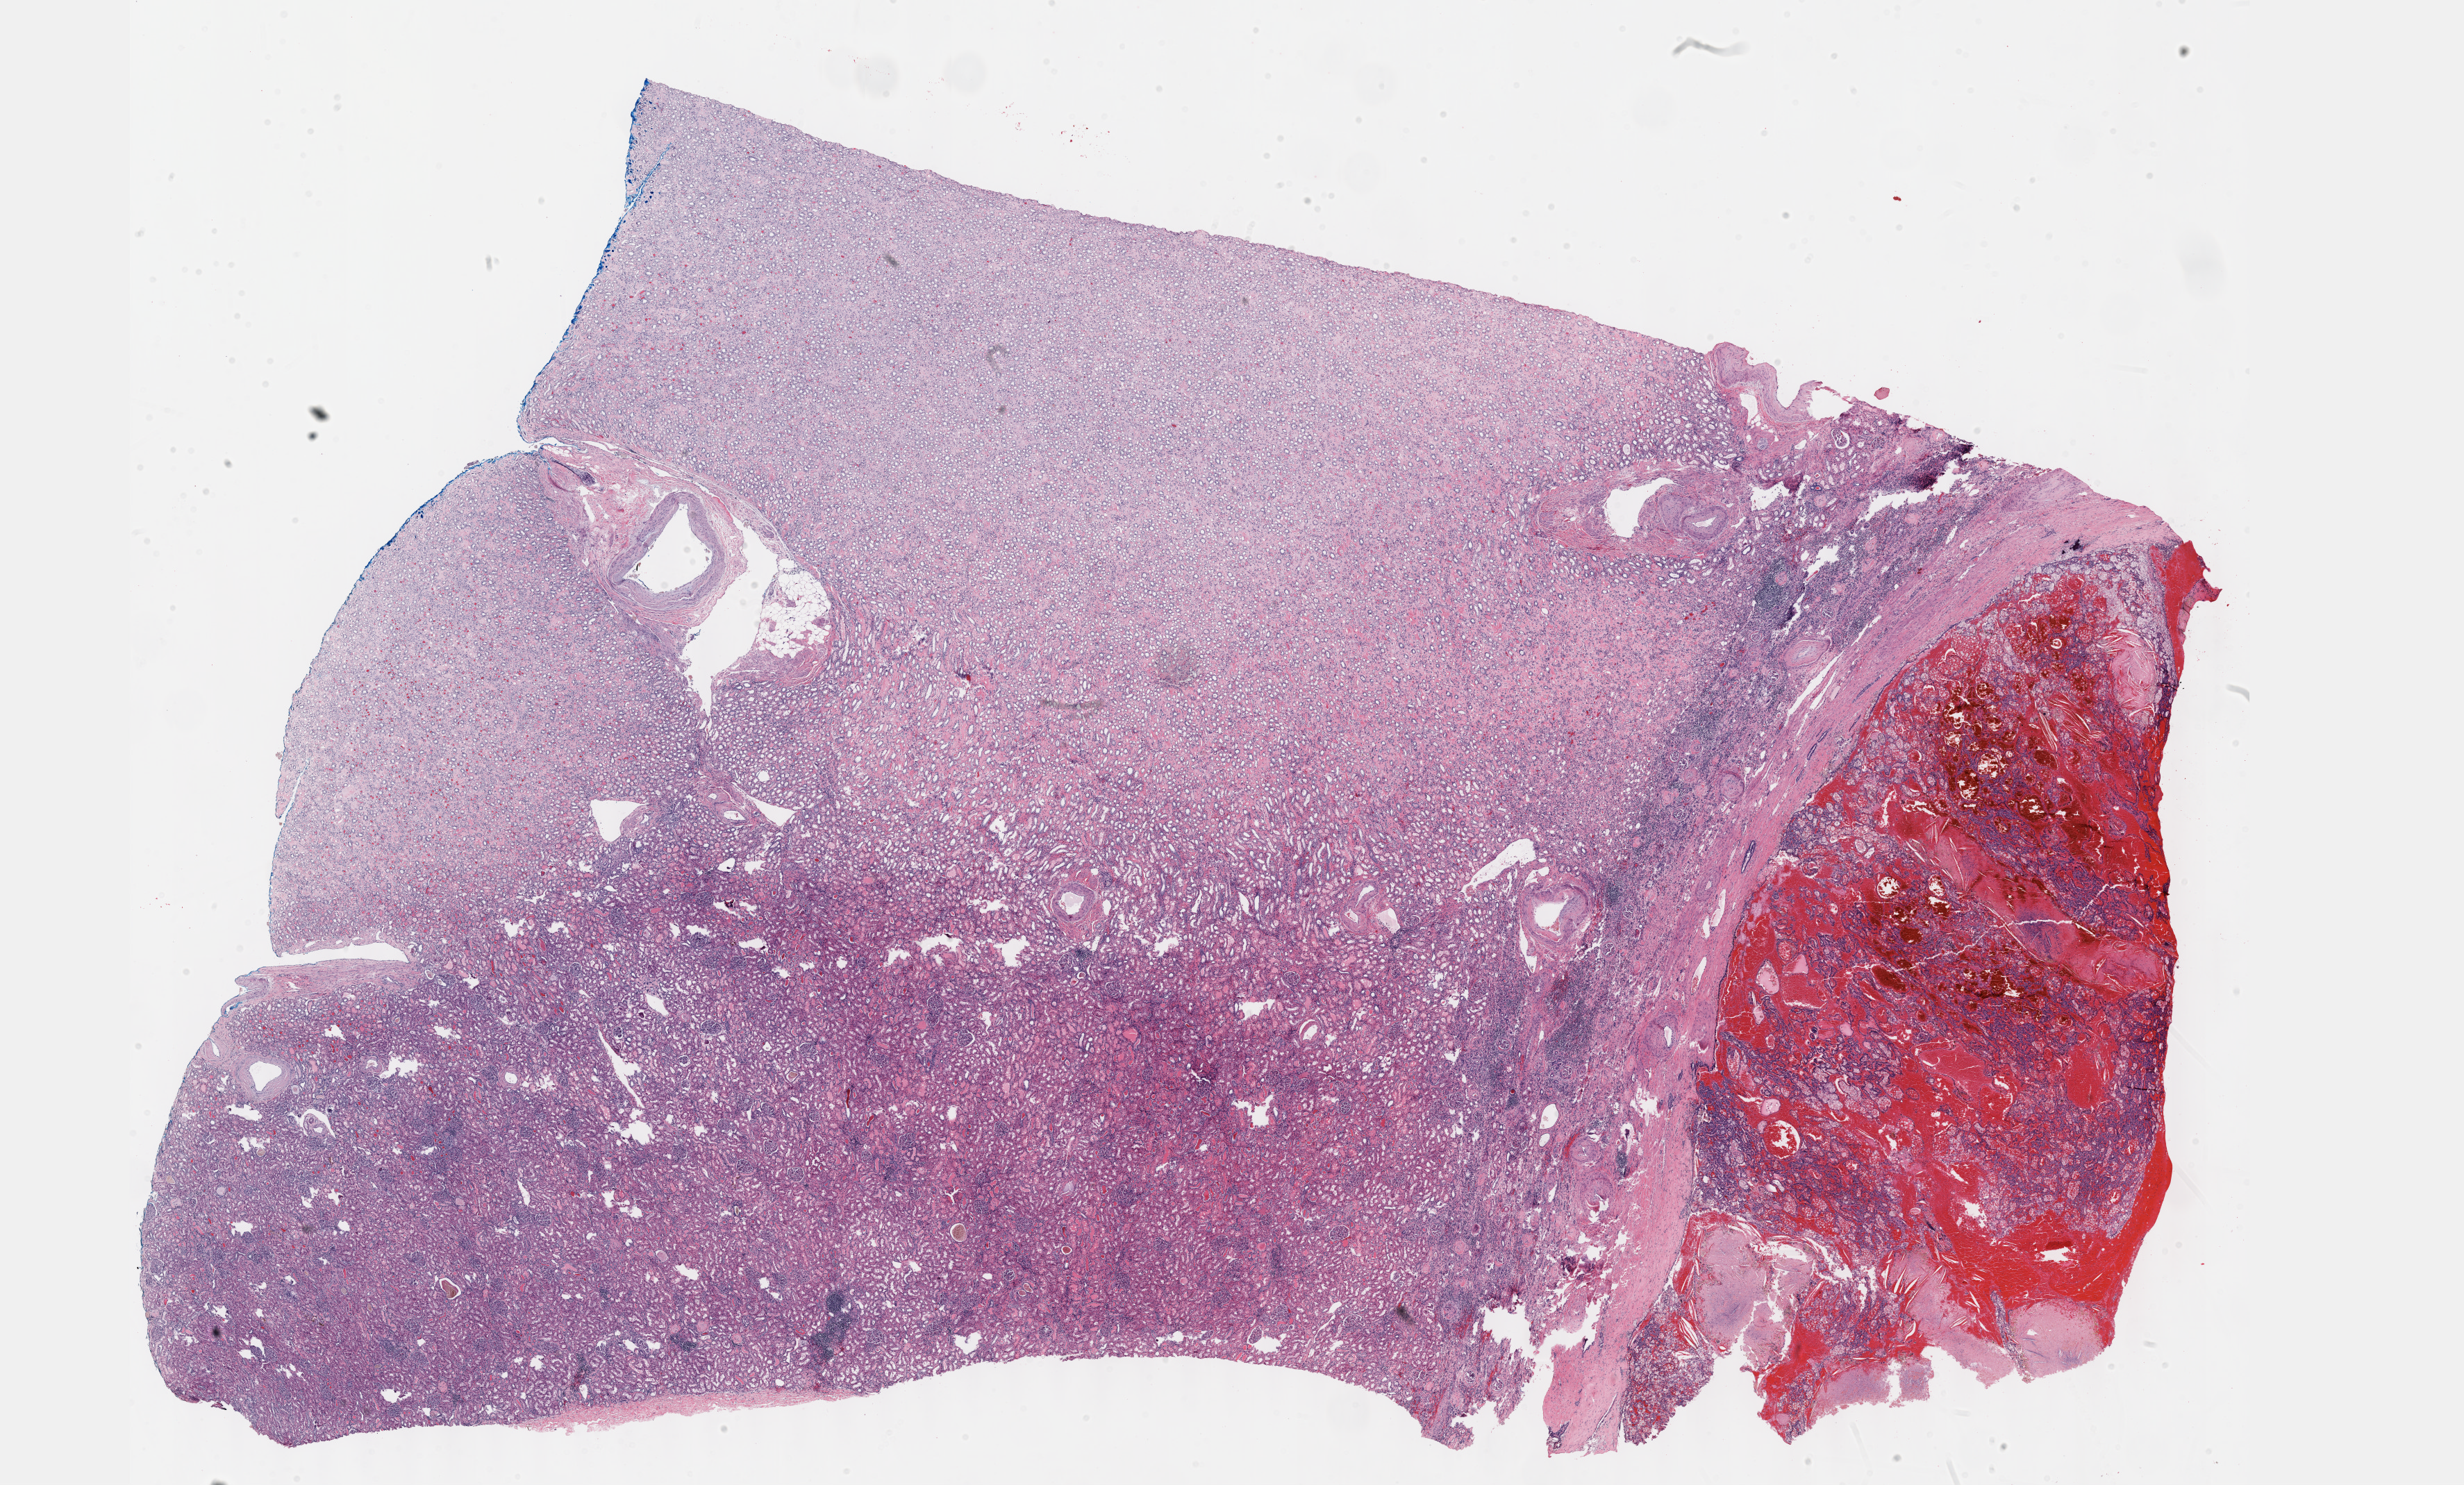
Hematoxylin and eosin (H&E) stained whole-slide image — a low-resolution overview of the entire scanned area, about 28.7 x 17.3 mm; FFPE section; sample: primary tumour, kidney. Patient: male, age at initial diagnosis 85 years.
- AJCC pathologic stage: I (7th edition)
- laterality: right
- histologic diagnosis: Papillary adenocarcinoma, NOS